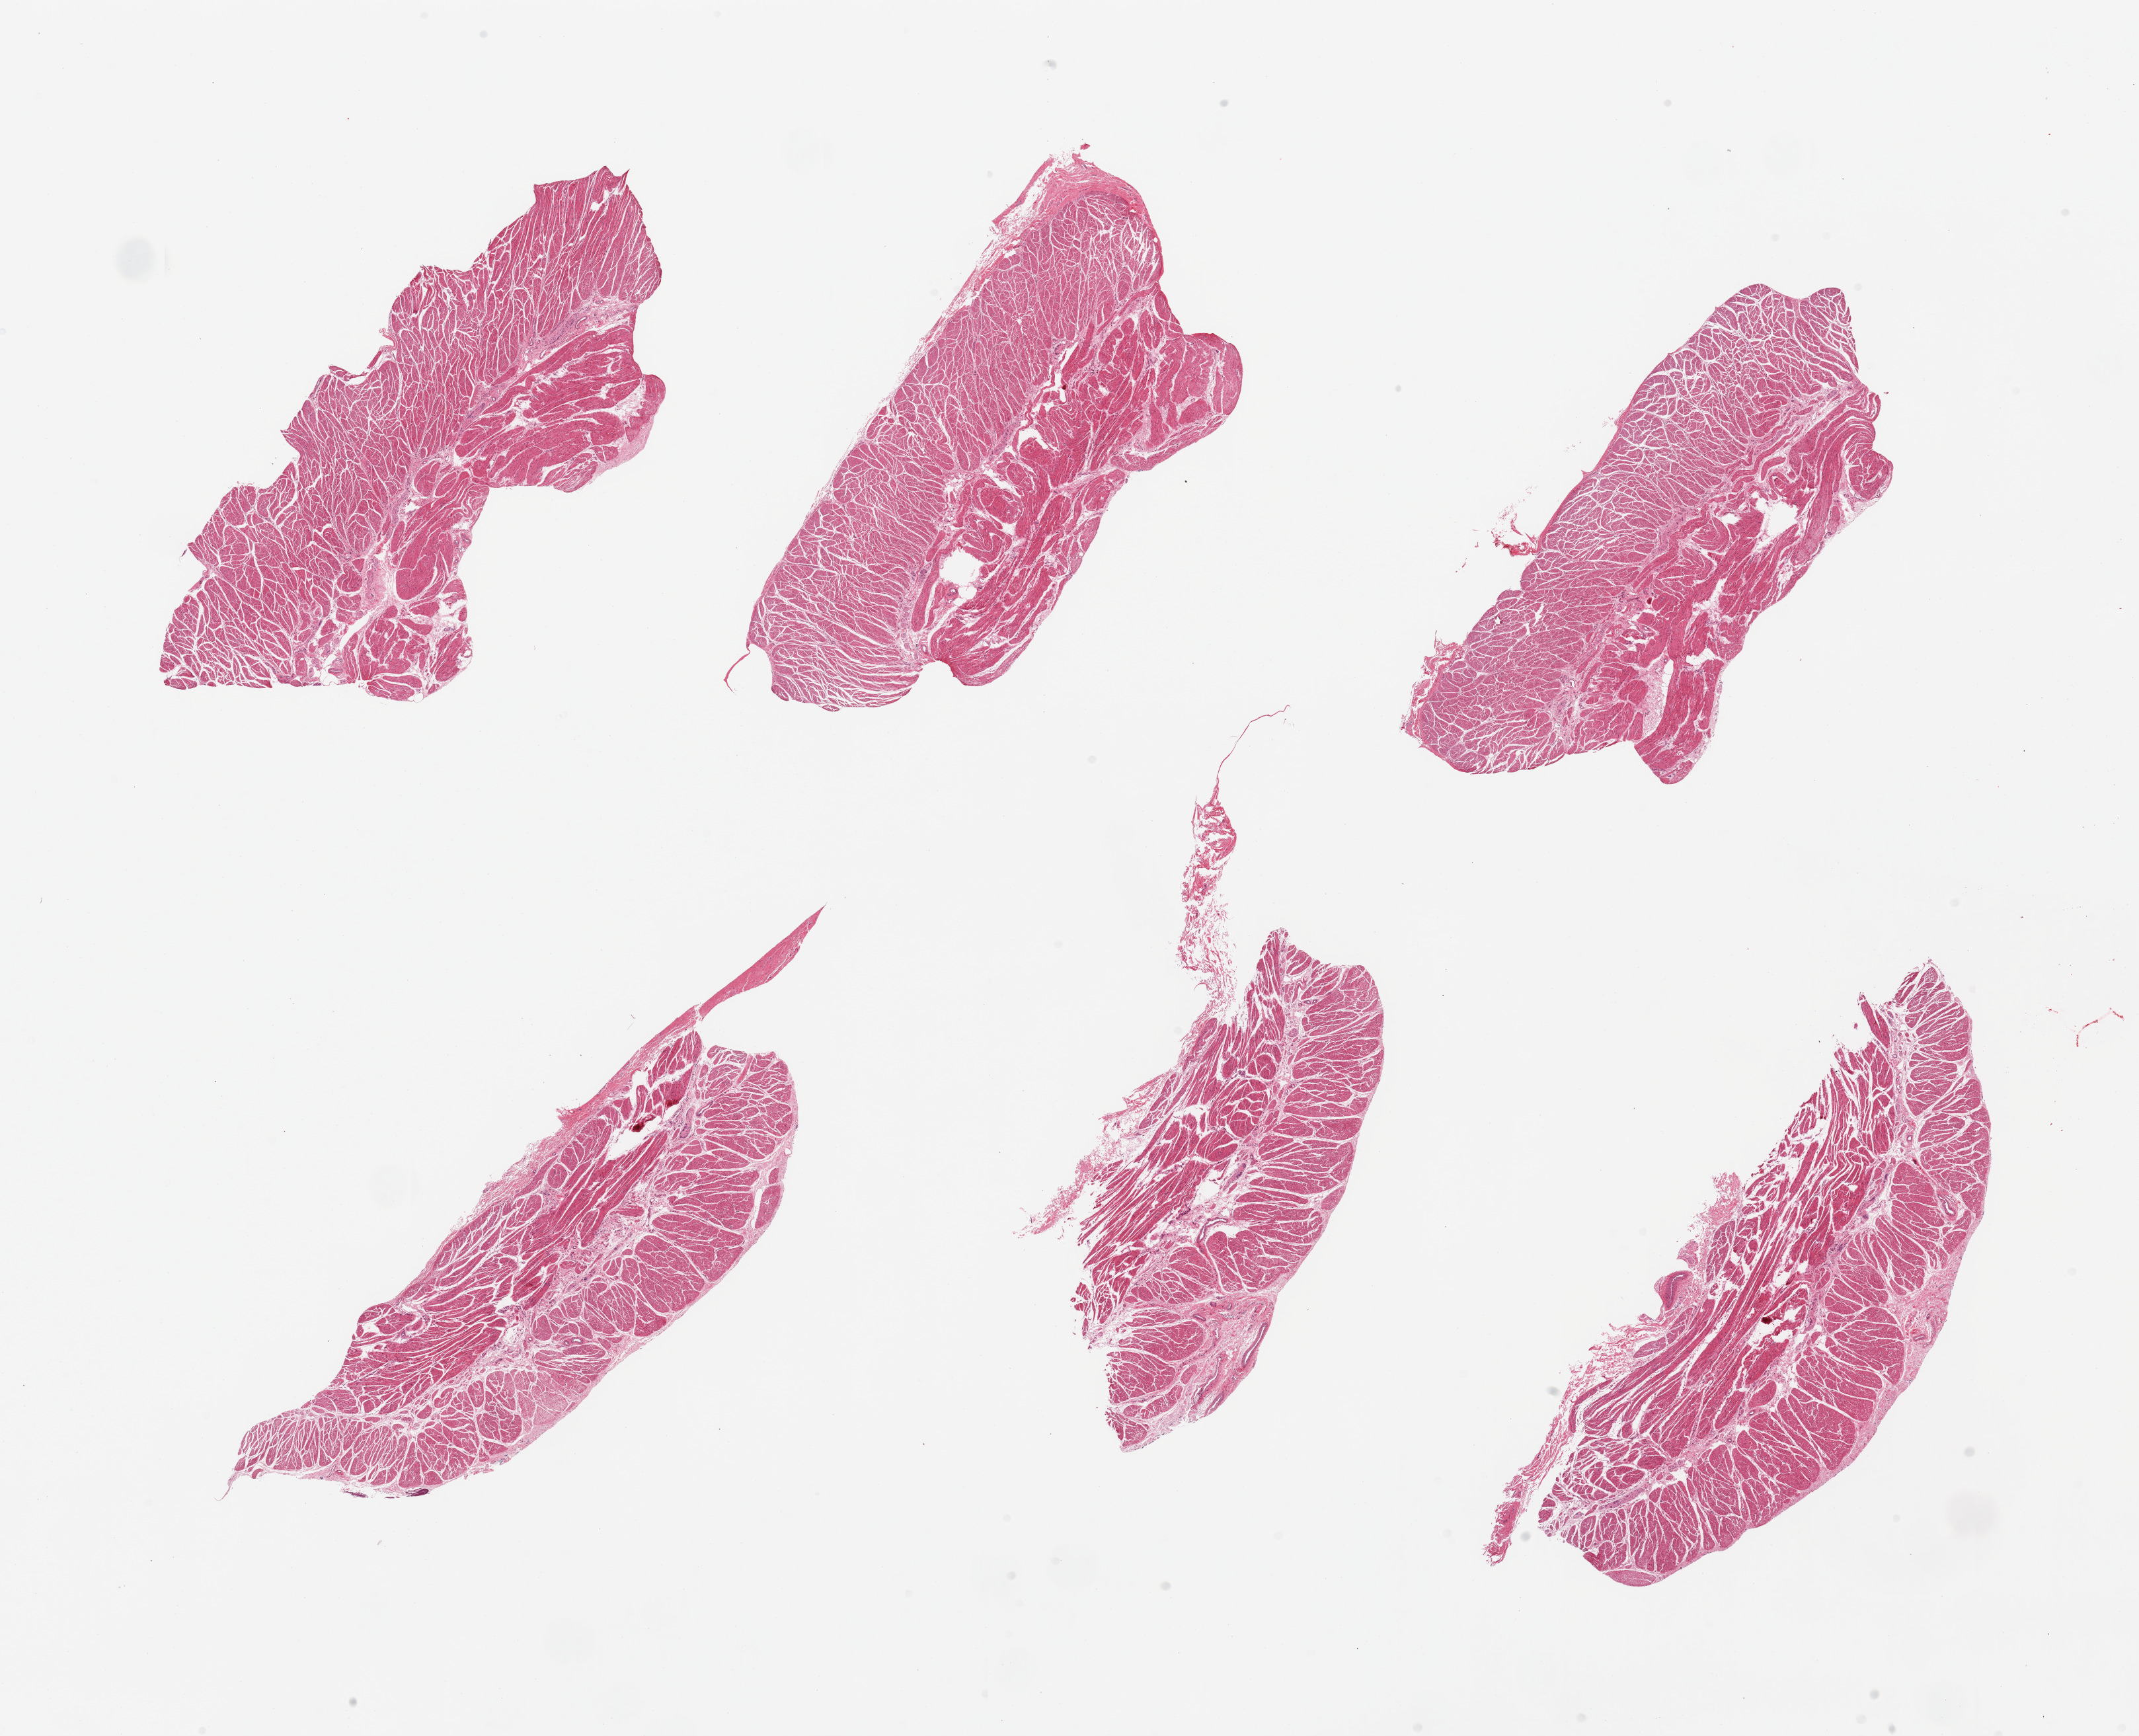
Whole-slide image, haematoxylin and eosin stain — shown as a low-resolution overview of the whole scanned area (about 25.6 x 20.8 mm, slide scanned at 20x); PAXgene-fixed, paraffin-embedded tissue; sampled site (target tissue): esophageal muscle; tissue donor sample. Donor sex: female.
Review note (as recorded): 6 pieces; well trimmed.